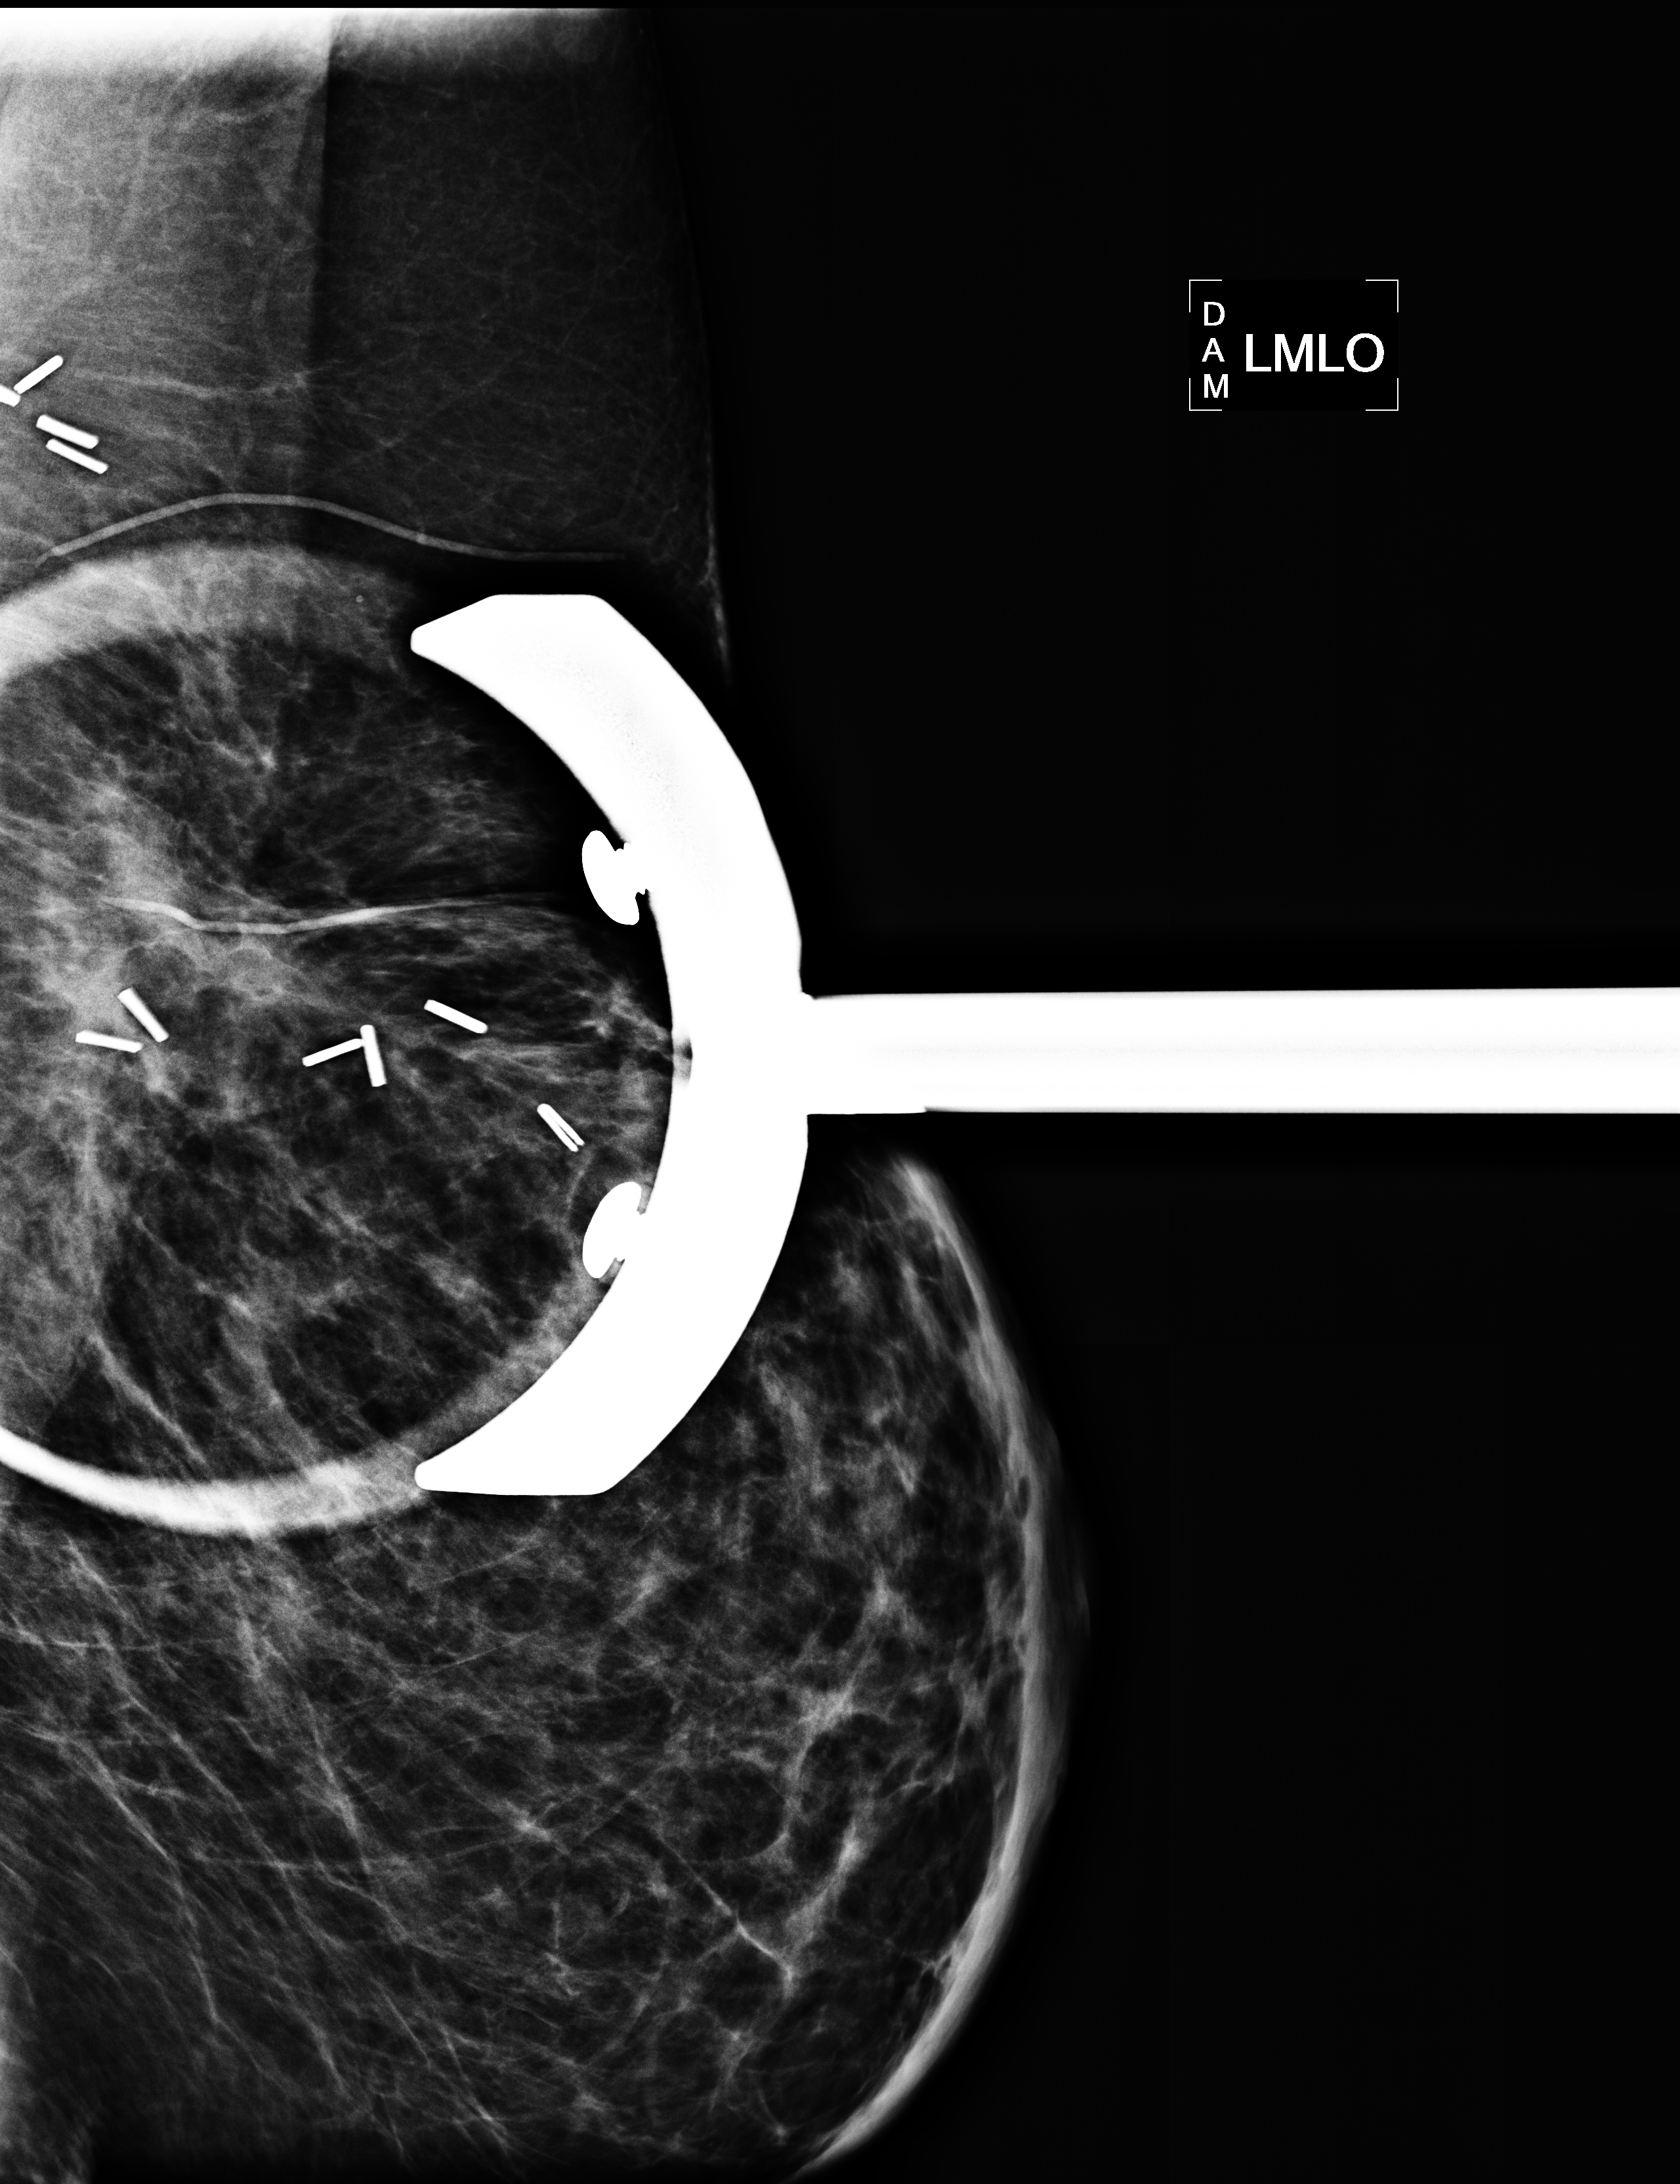
Mammogram, left breast, MLO view; patient in her 50s.
Patient-level pathology facts (clinical record, not image findings): pathology diagnosis: Invasive ductal CA (left breast); receptor status (as recorded): ER pos, PR pos (weak), HER2 neg; Ki-67 (as recorded): intermed prolif; pathology report notes: re-bx [date] was scar tissue from RT rx.